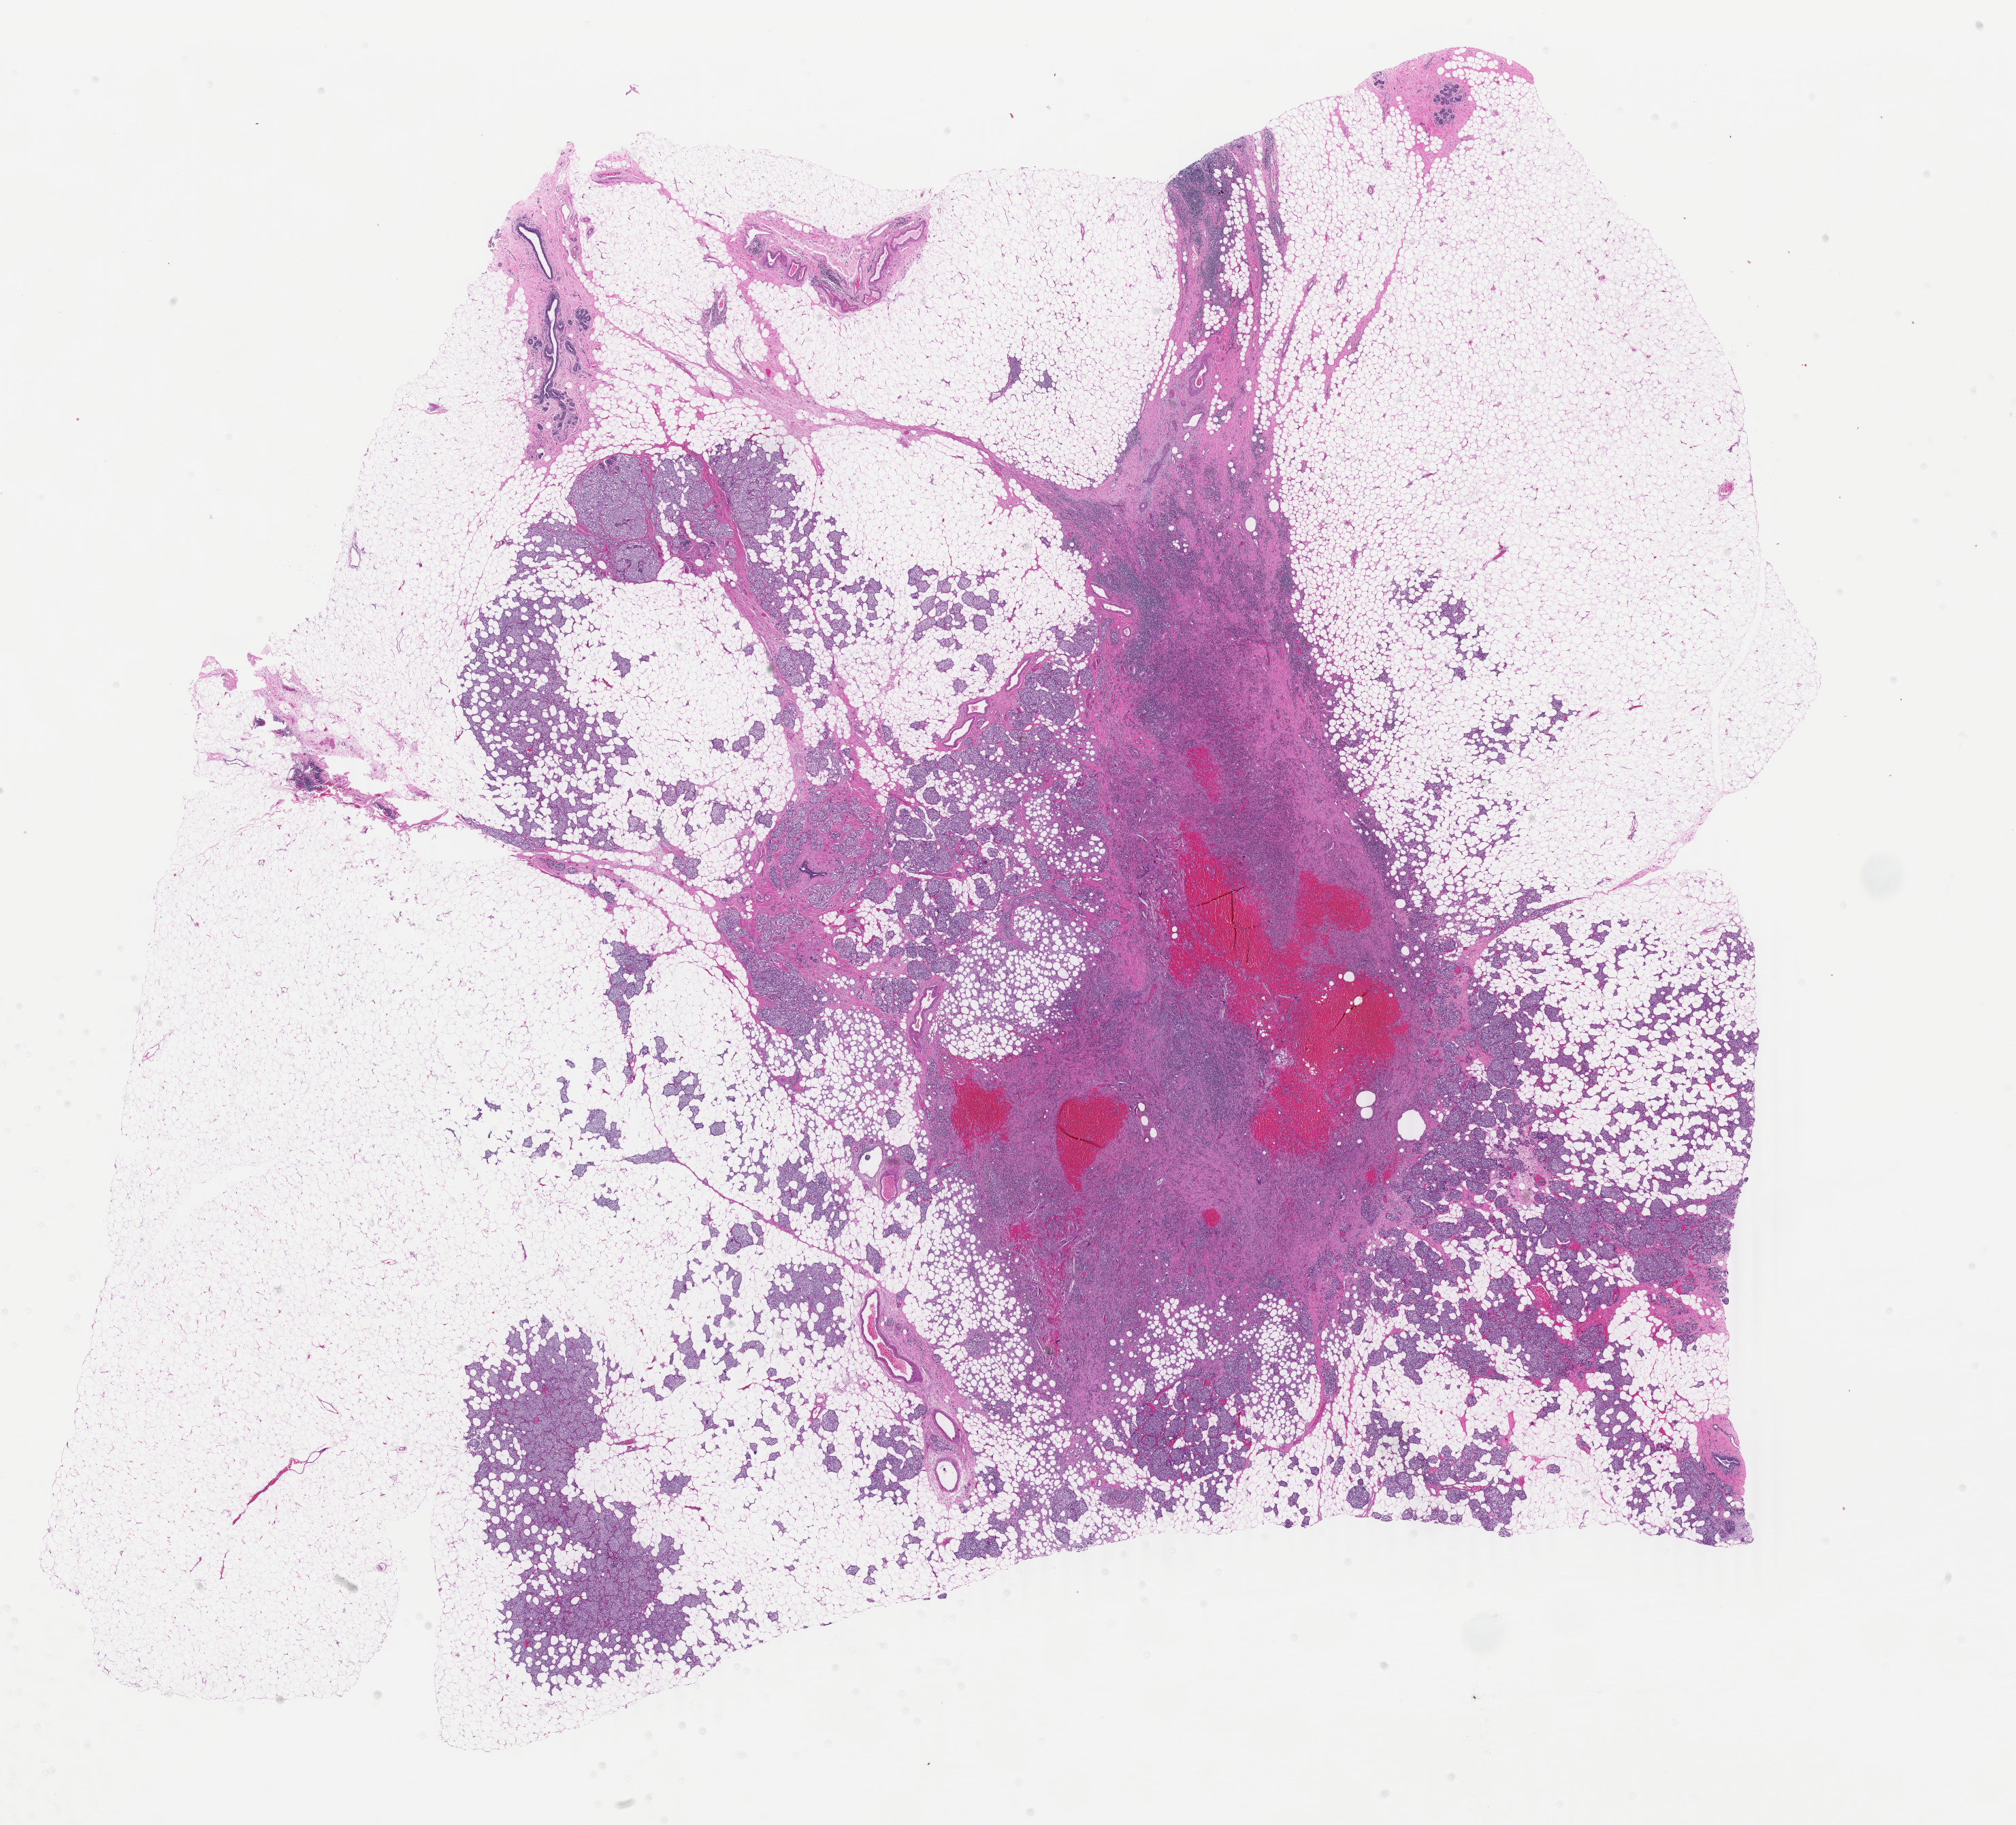
Whole-slide histology image, Hematoxylin and eosin (H&E) stained, low-resolution overview of the scanned area, about 23.6 x 21.3 mm (acquisition: 40x scan); FFPE section; primary tumour sample from the breast. Female, age 37 years at initial diagnosis.
- lymph nodes positive (case pathology): 1 of 23 examined
- diagnosis: Infiltrating duct carcinoma, NOS
- AJCC pathologic stage: IIB (6th edition)